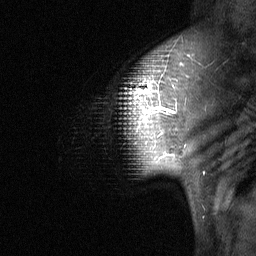
Breast MRI (dynamic contrast-enhanced), one sagittal slice. Position 50 of 64 along the scan axis. Dynamic contrast-enhanced study with each time point stored as its own series, time point 2 of 3 at this slice position (early post-contrast, ordered by acquisition time). 1.5 T. TE 4.8 ms, TR 27 ms. 256 × 256 image matrix, field of view 200 × 200 mm. Patient: female, 42 years. From the clinical record (not read from this slice): setting: breast cancer imaged before/during neoadjuvant chemotherapy; receptor status: triple-negative.
Structures marked on this image (semi-automatic segmentation, software-assisted and operator-edited):
- analysis volume of interest (the breast-tissue region the enhancement analysis was run in; not a lesion): bounding box [x1, y1, x2, y2] px = [124, 41, 203, 190]
- tumour enhancement mask (voxels above the 90 % enhancement threshold inside the analysis volume of interest): [130, 83, 175, 129]